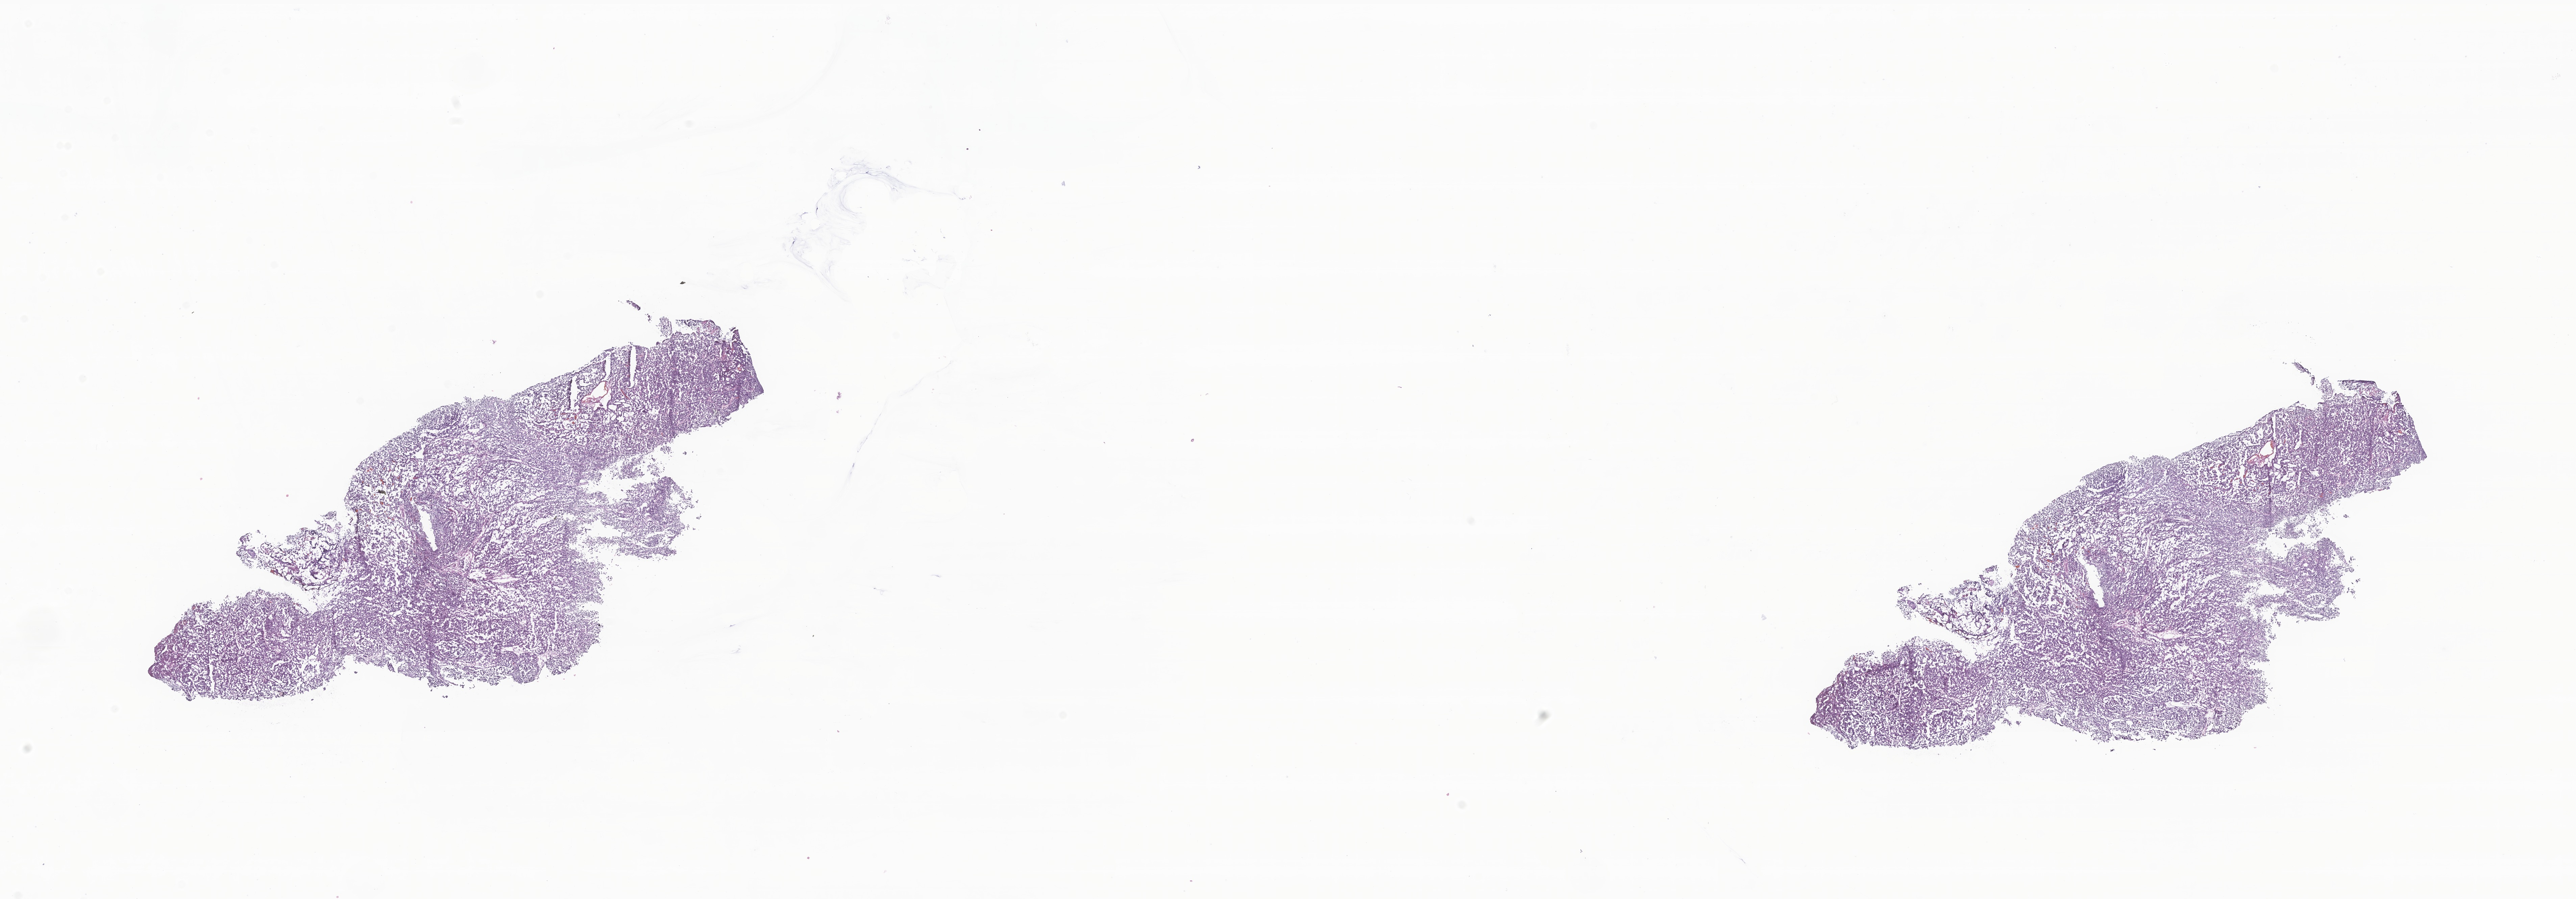
Hematoxylin and eosin (H&E) whole-slide image of tumor tissue from the occipital lobe, shown as a low-resolution overview of the whole scanned area (about 32.1 x 11.2 mm); frozen section (OCT-embedded). Male patient, age 46 months (3 years 10 months).
- diagnosis: Medulloblastoma, NOS